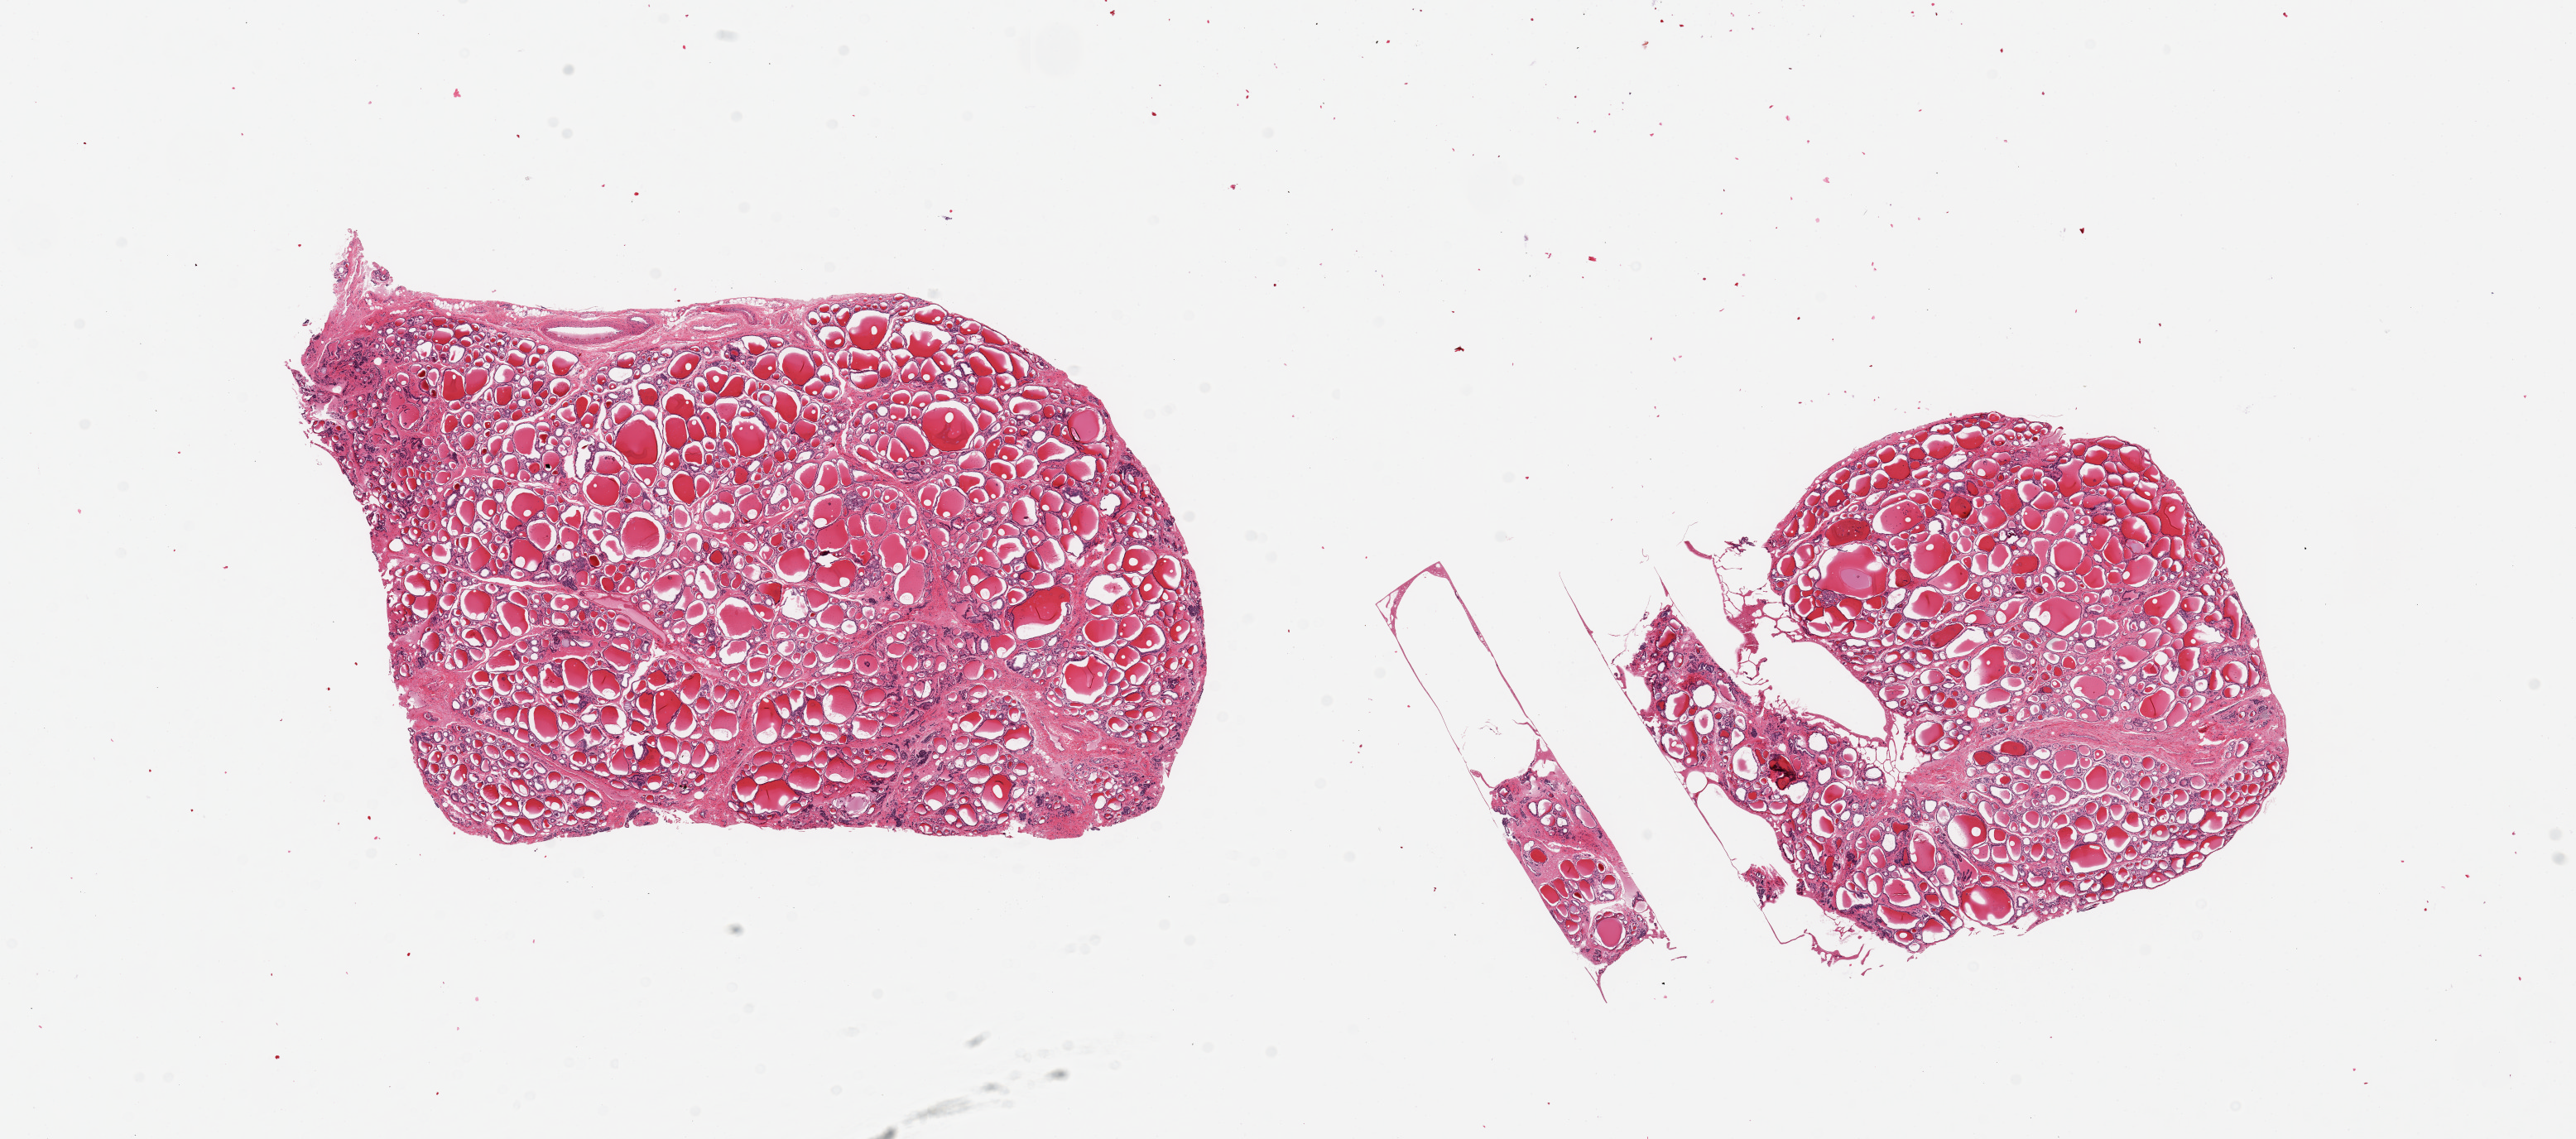
Digitized hematoxylin and eosin (H&E)-stained section, brightfield — low-resolution overview of the scanned area, about 24.6 x 10.9 mm (from a 20x scan), PAXgene-fixed paraffin-embedded (PFPE) section, section of thyroid (target tissue), donor tissue sample. Donor sex: male.
- review note (as recorded): 2 pieces, 9x6 & 7x5mm; nodular goitre with fibrous bands noted